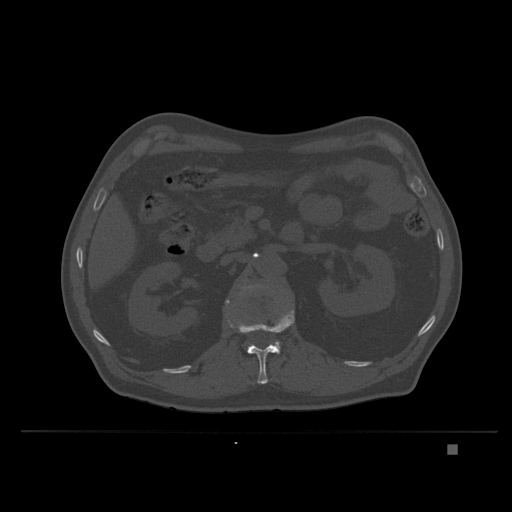
CT including the spine, one axial slice; position 132 of 435 along the scan axis; bone window (W 1800 / L 400 HU); 1.5 mm slice thickness; 512 × 512 image matrix, field of view 434 × 434 mm. Patient: male, 73 years. Case-level facts recorded for this patient, not image findings: primary cancer: skin.
Outlined on this slice (semi-automatic segmentation, software-assisted and operator-edited):
- L1 vertebra: bounding box (x1, y1, x2, y2) in pixels: (227, 308, 295, 384)
- L2 vertebra: (248, 286, 252, 289)